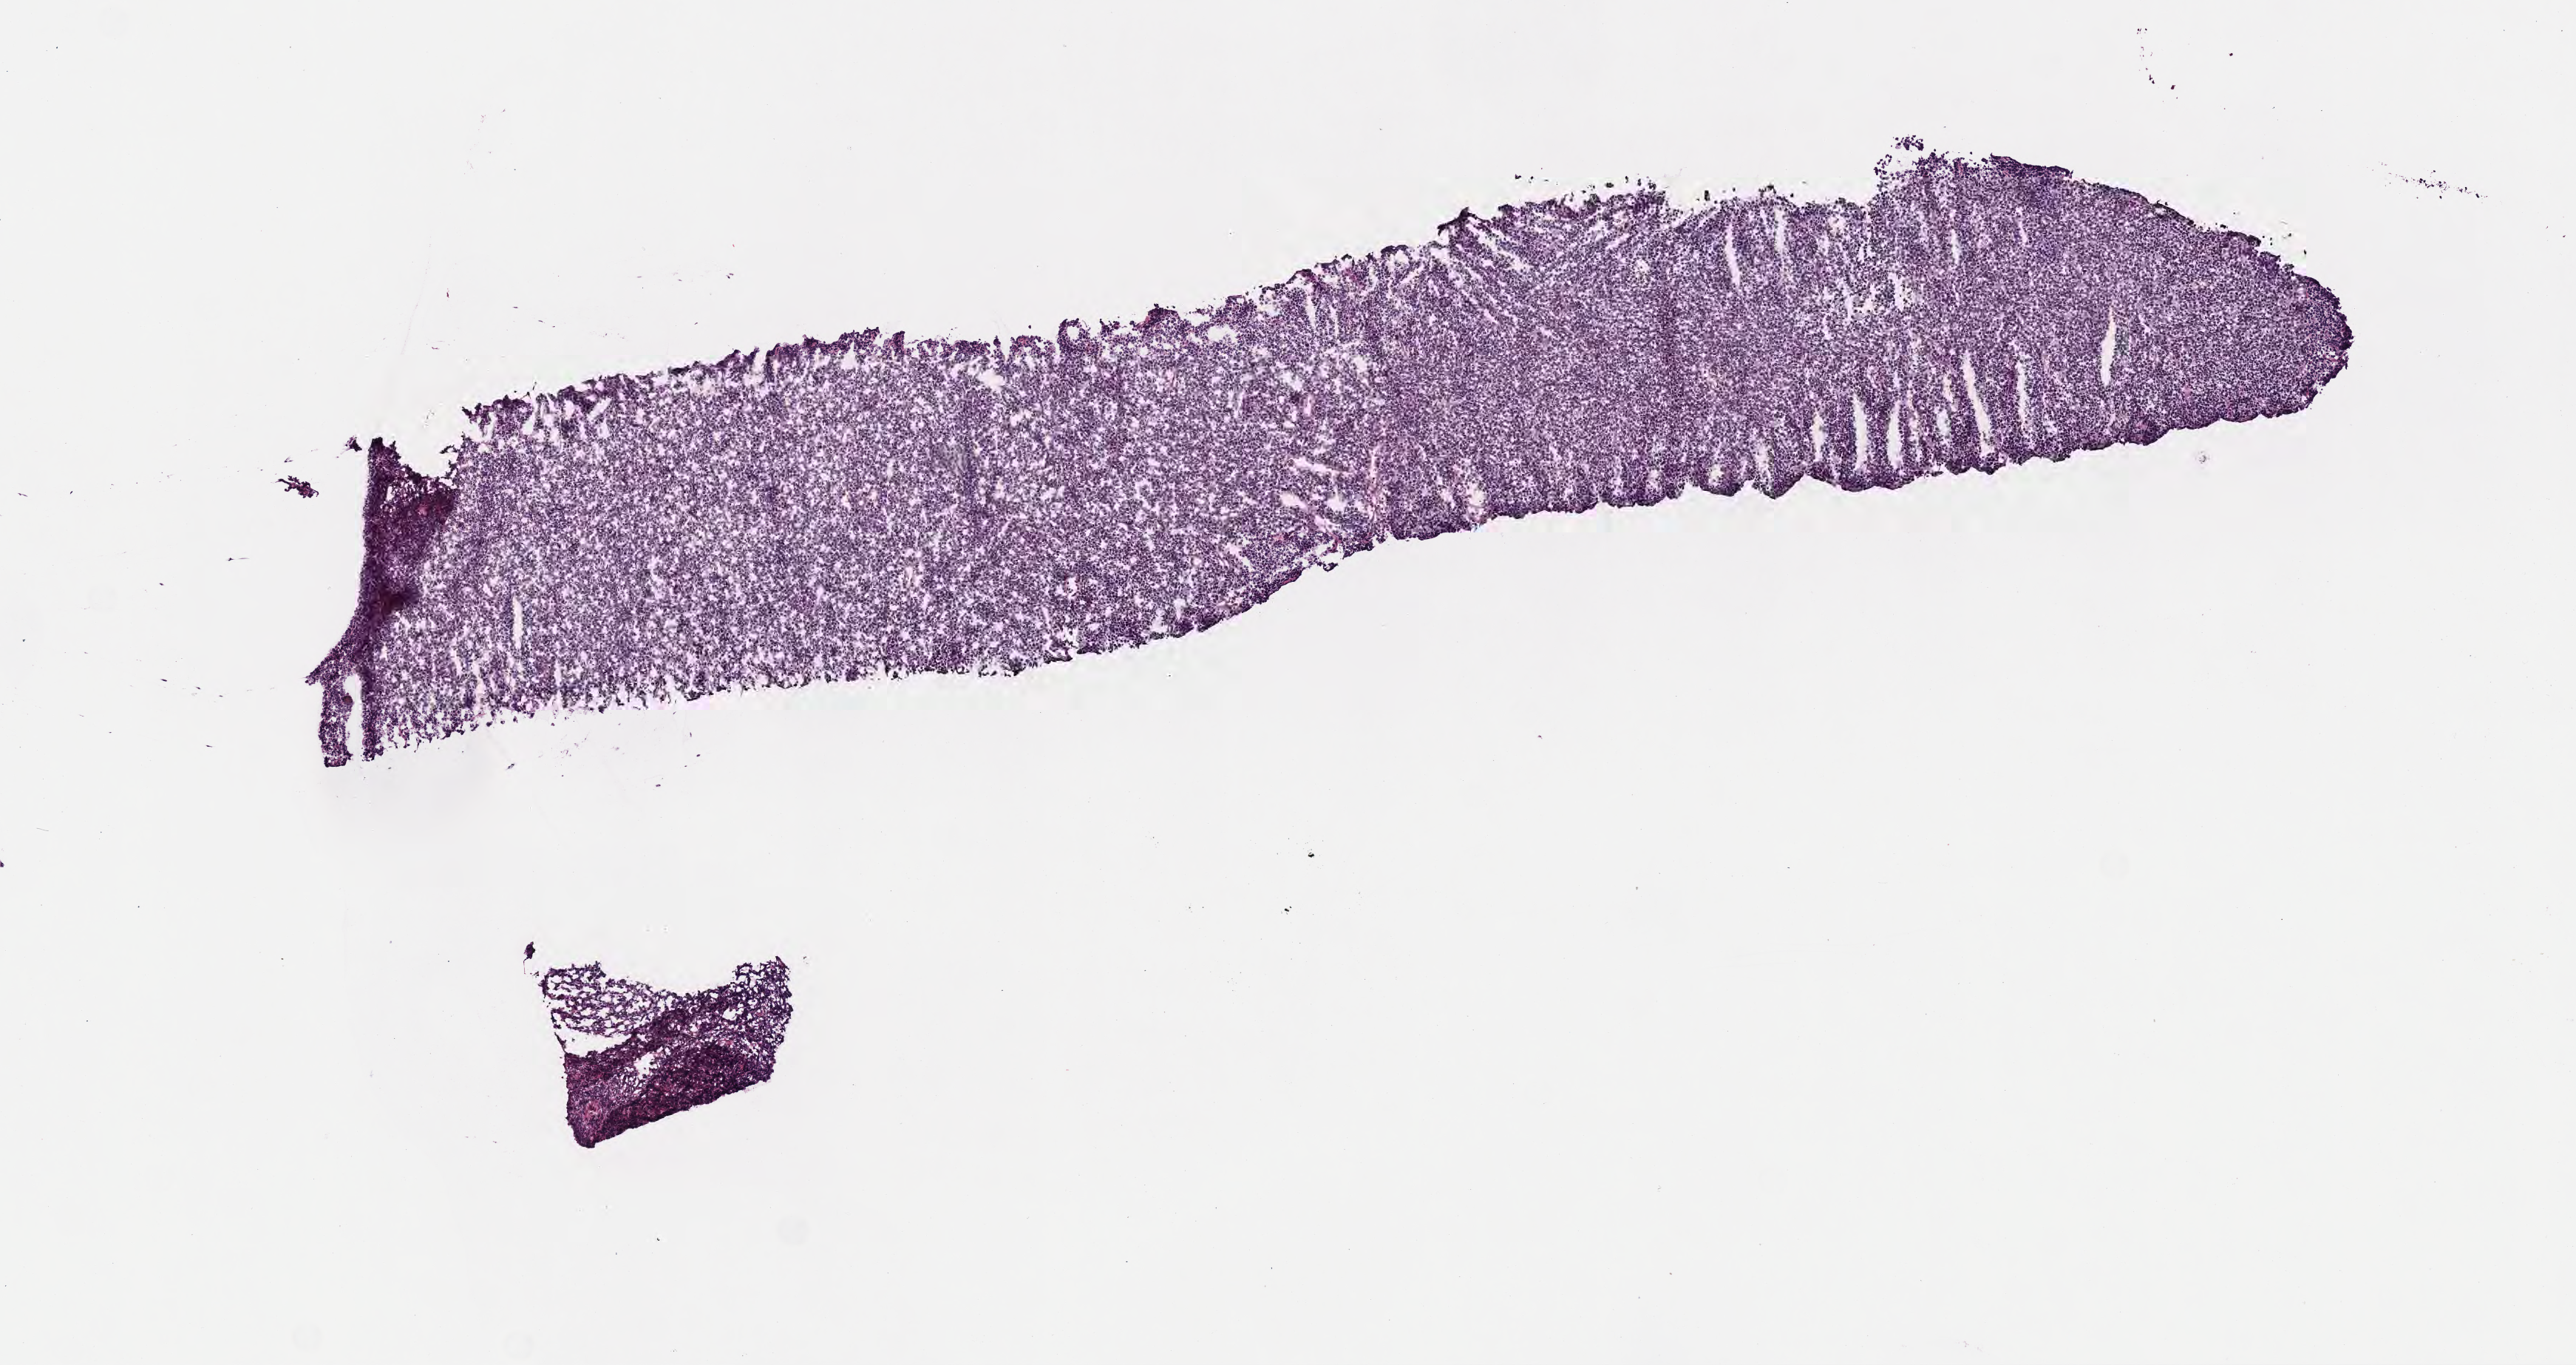
Digitized hematoxylin and eosin (H&E)-stained section, shown as a low-resolution overview of the whole scanned area (about 7.0 x 3.7 mm); cryosection; primary tumor; site: liver. Patient: male, age at initial diagnosis 4 years. Slide review estimates, as recorded: tumor cells 90%, tumor nuclei 95%, stromal cells 5%, necrosis 5%, normal cells 0%. Inflammatory infiltration, as recorded: lymphocyte infiltration 10%, monocyte infiltration 30%, neutrophil infiltration 10%.
Ann Arbor stage (patient): Stage III. Histologic diagnosis: Burkitt lymphoma, NOS.